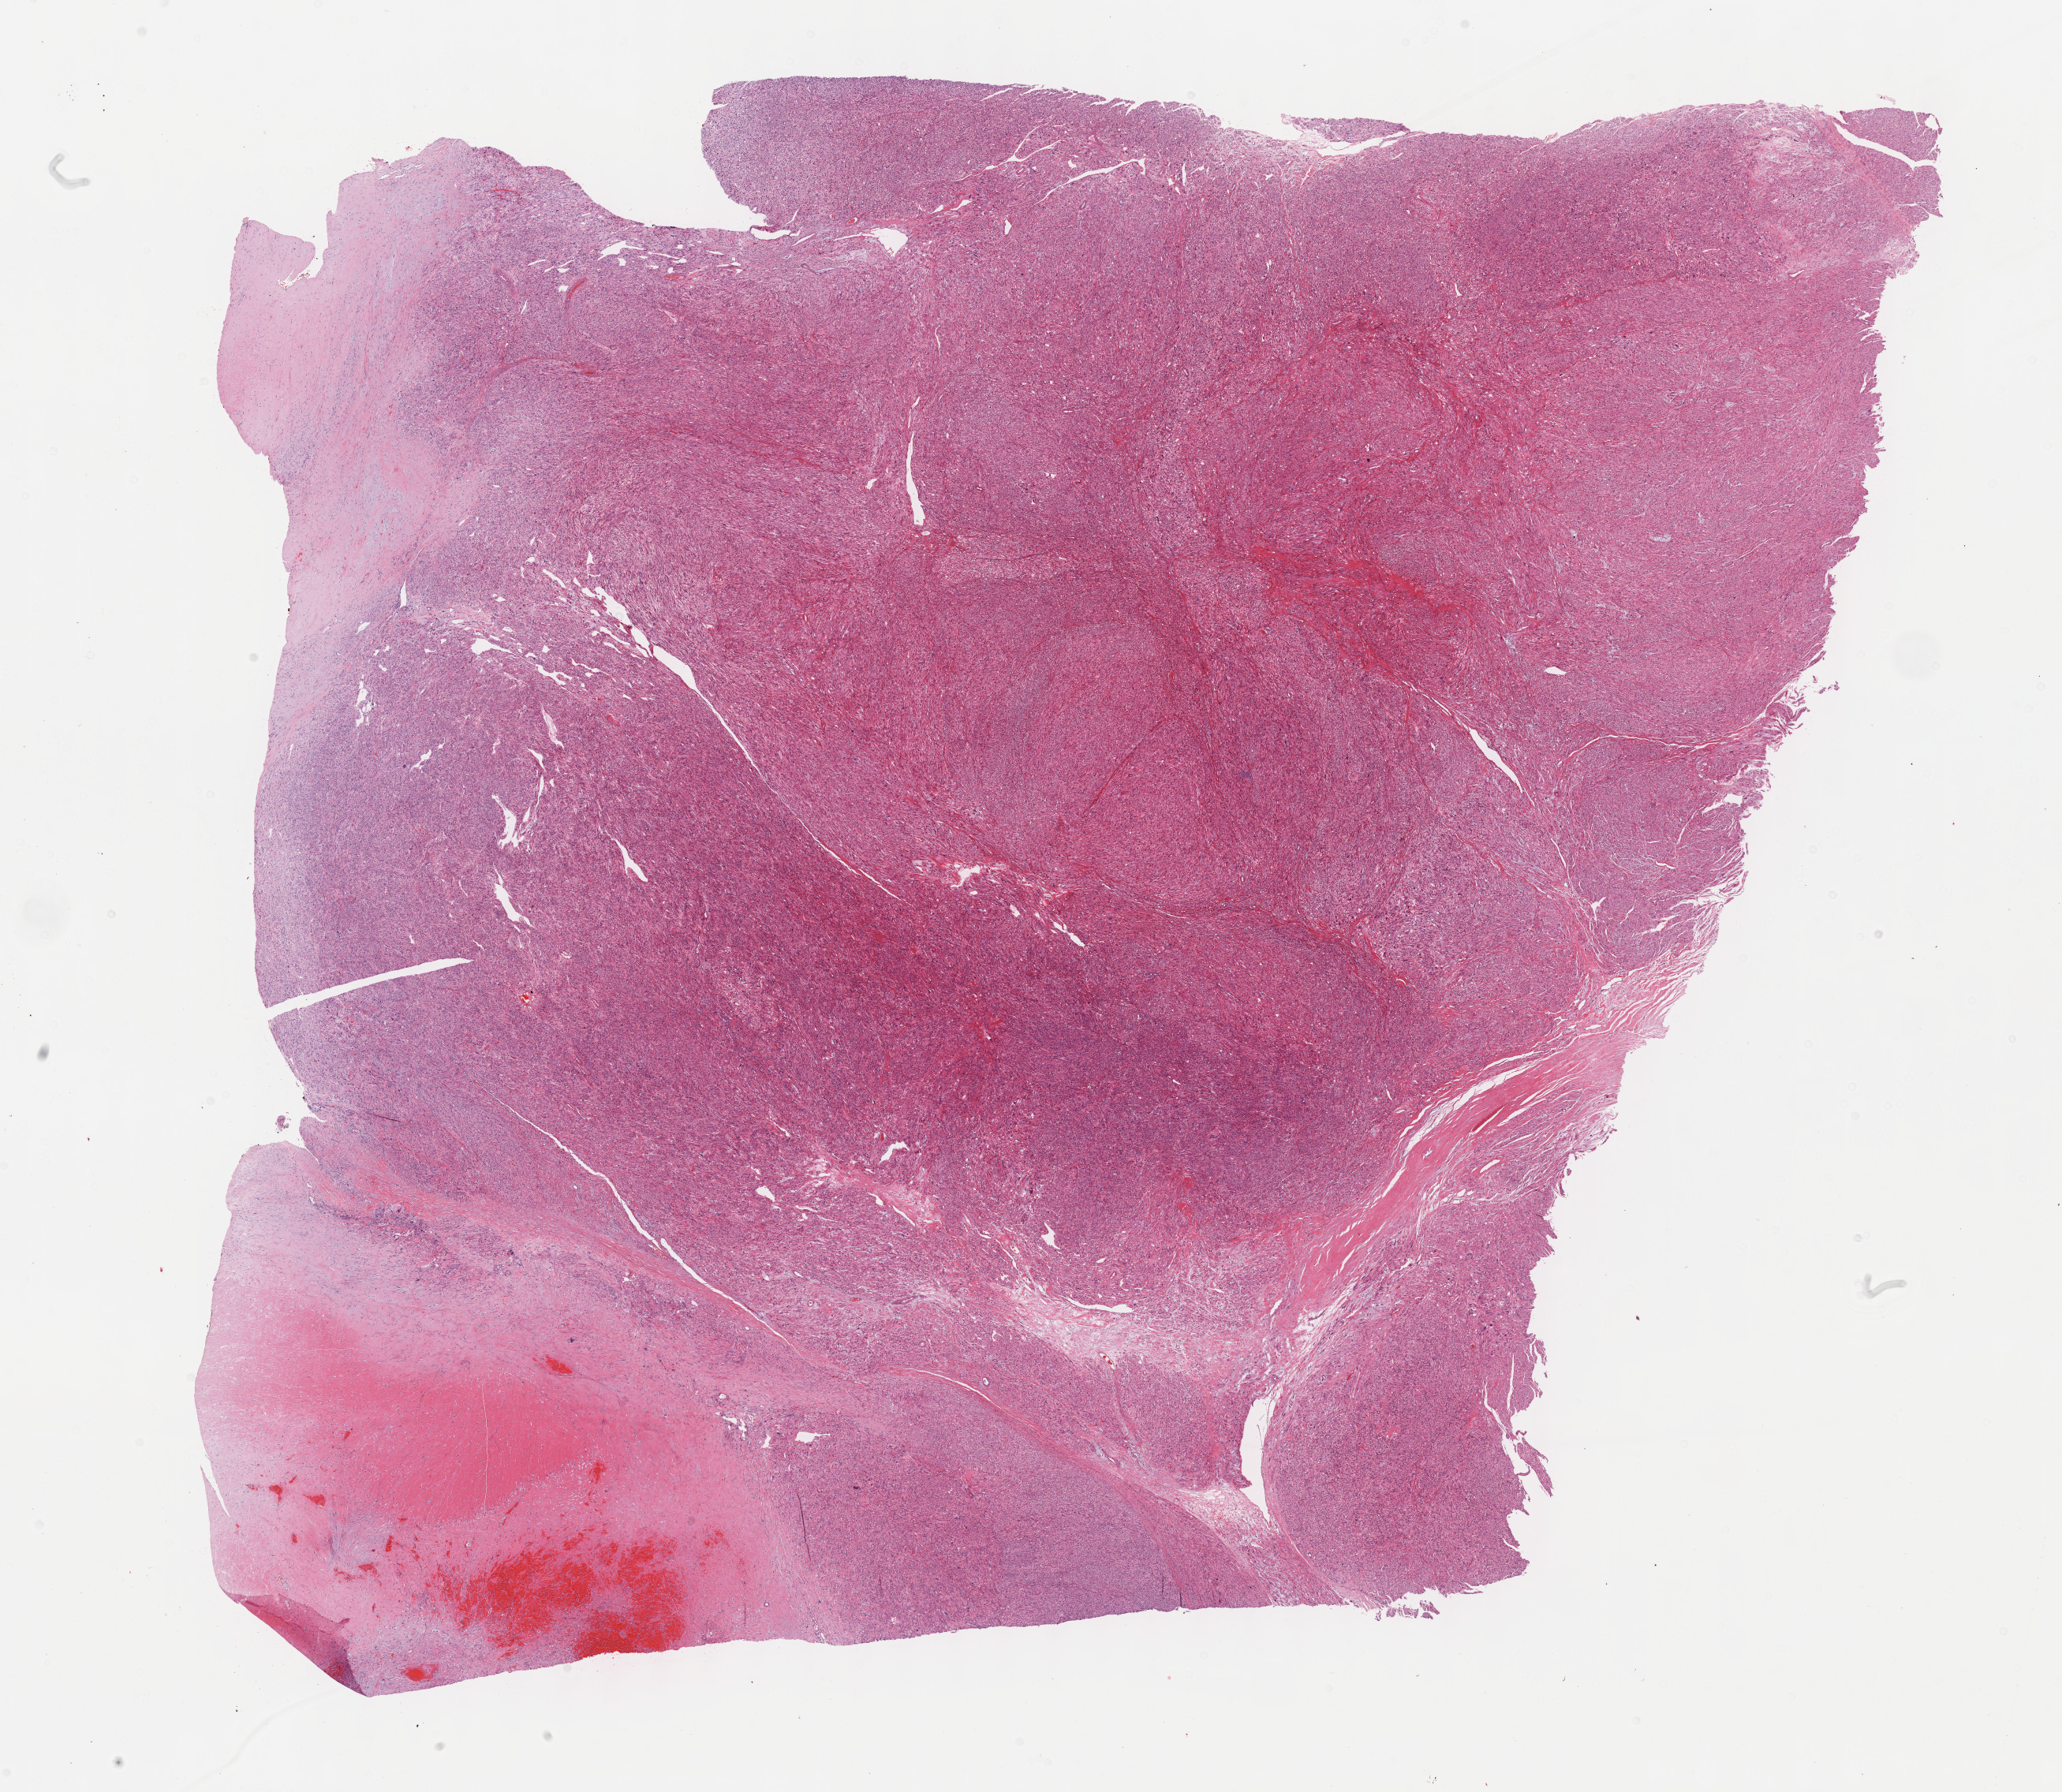
Hematoxylin and eosin (H&E) stained whole-slide image, whole scanned area (about 21.1 x 18.4 mm, slide scanned at 40x) shown as a low-resolution overview; formalin-fixed paraffin-embedded (FFPE) diagnostic section; sample: primary tumour, connective, subcutaneous and other soft tissues. Female, age 56 years at initial diagnosis.
Diagnosis: Leiomyosarcoma, NOS (connective, subcutaneous and other soft tissues of abdomen).